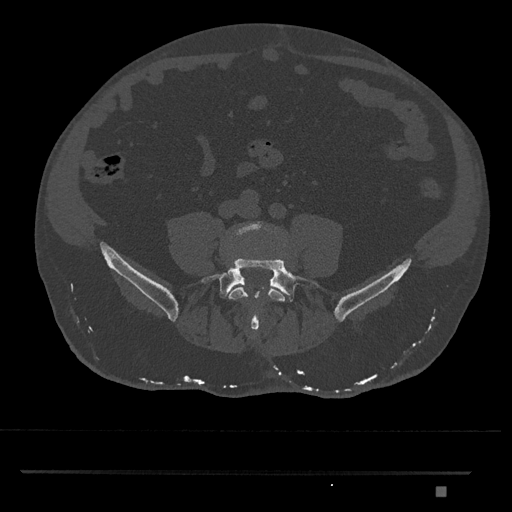
CT including the spine, one axial slice; slice 577 of 1134 in the series (ordered by position); reconstruction kernel Br40s/3; 120 kVp; bone window (W 1800 / L 400 HU); 0.5 mm slice thickness; 512 × 512 image matrix, field of view 429 × 429 mm. Male patient, age 65 years. Case-level facts recorded for this patient, not image findings: primary cancer: prostate.
Structures marked on this image (semi-automatically segmented with operator editing):
- L4 vertebra: bounding box (x1, y1, x2, y2) in pixels: (228, 221, 286, 322)
- L5 vertebra: (201, 258, 322, 332)